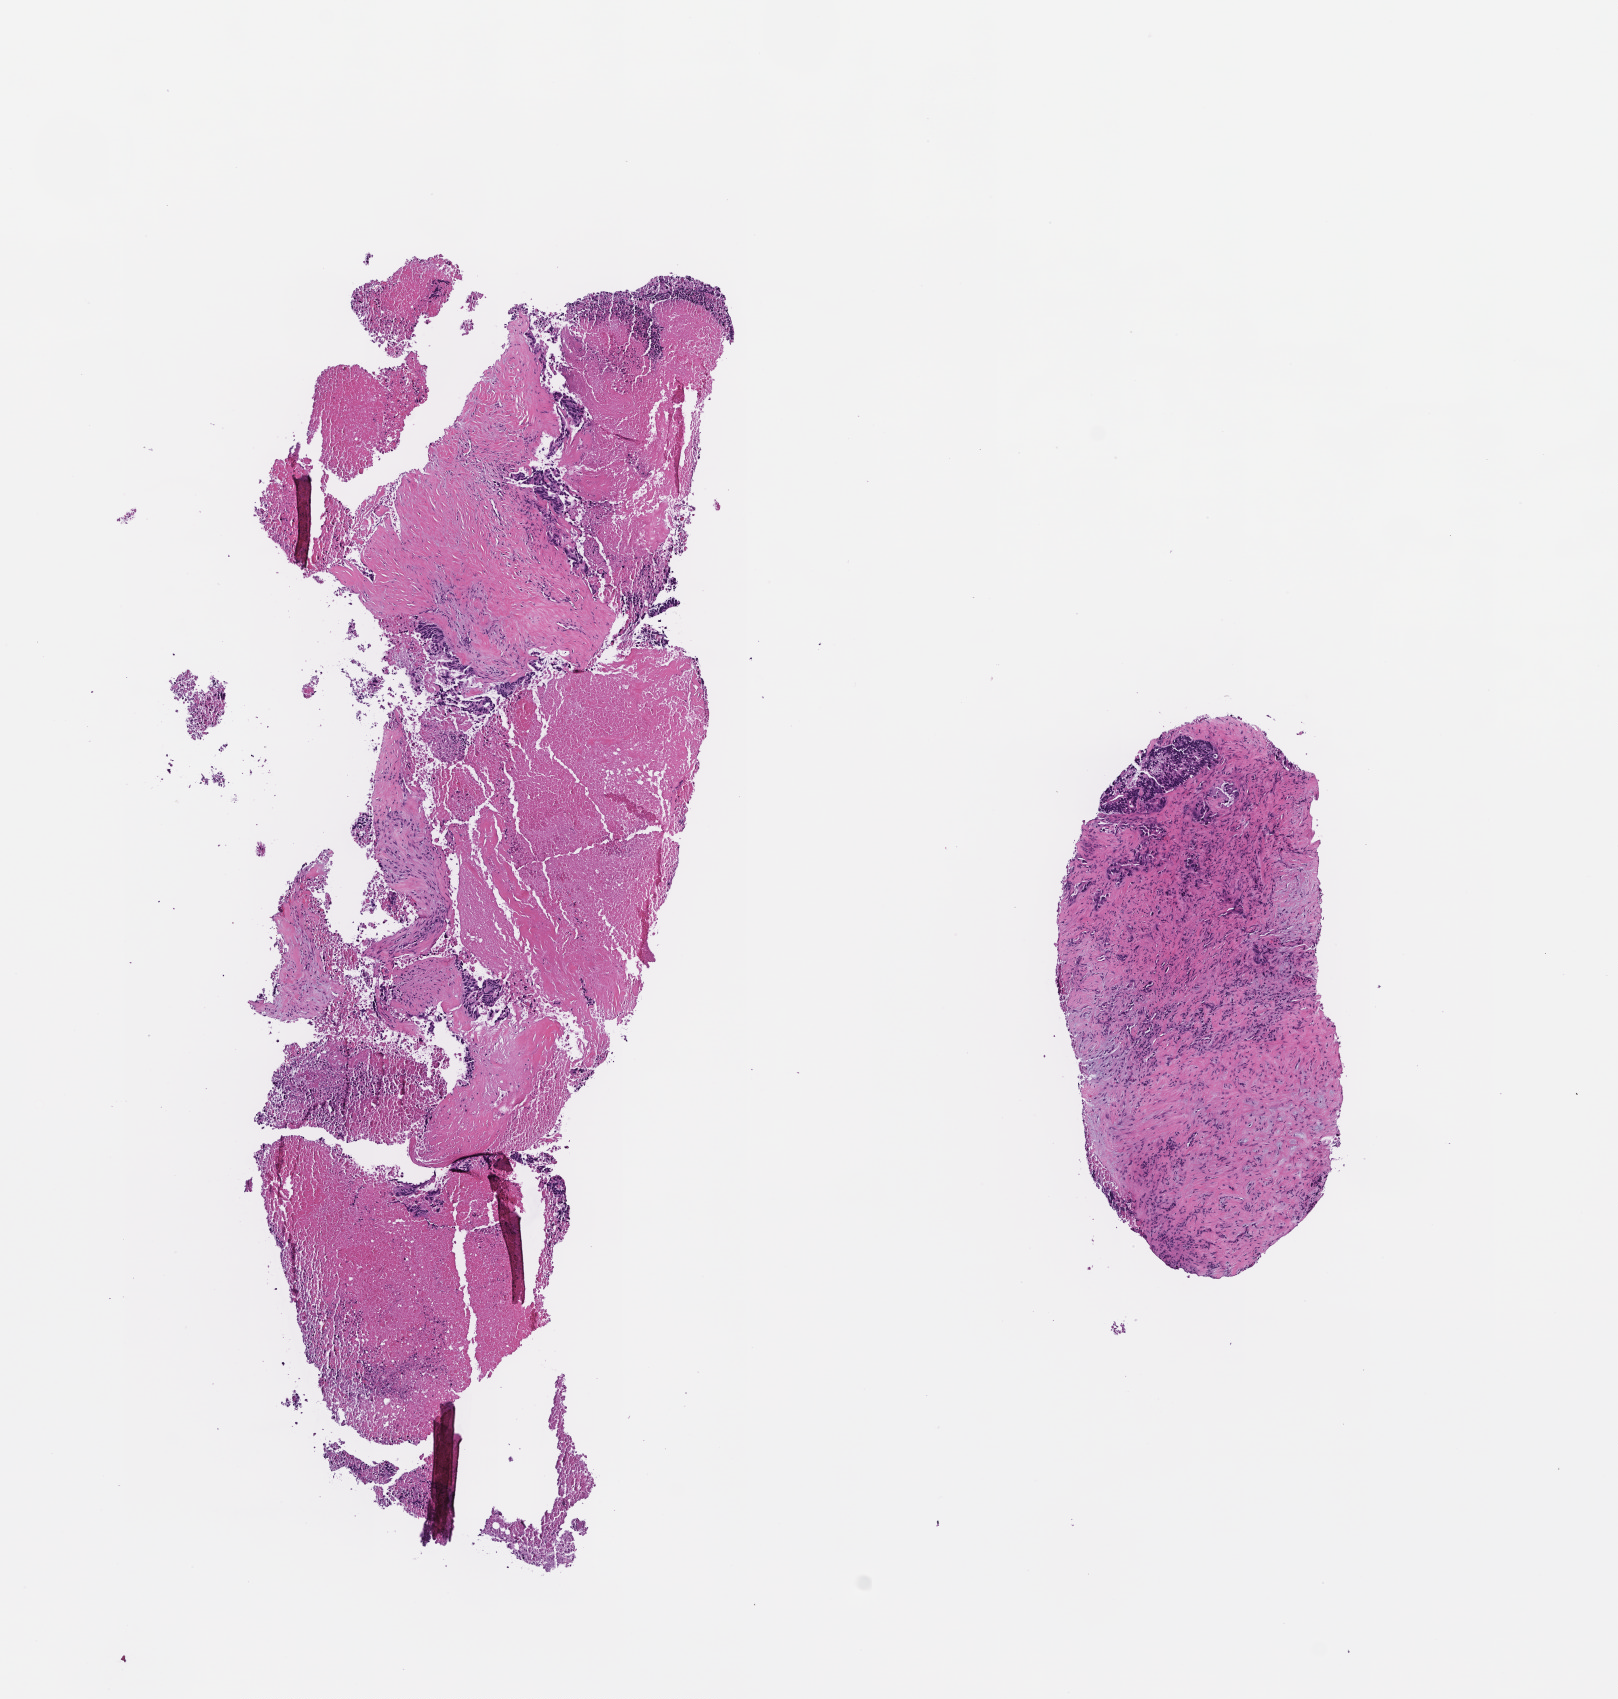
Whole-slide image, hematoxylin and eosin (H&E) stain, whole scanned area (about 6.5 x 6.9 mm) shown as a low-resolution overview, FFPE section. Patient: female.
• this section: metastasis (sampled organ not recorded)
• primary diagnosis of the patient: Colorectal Carcinoma